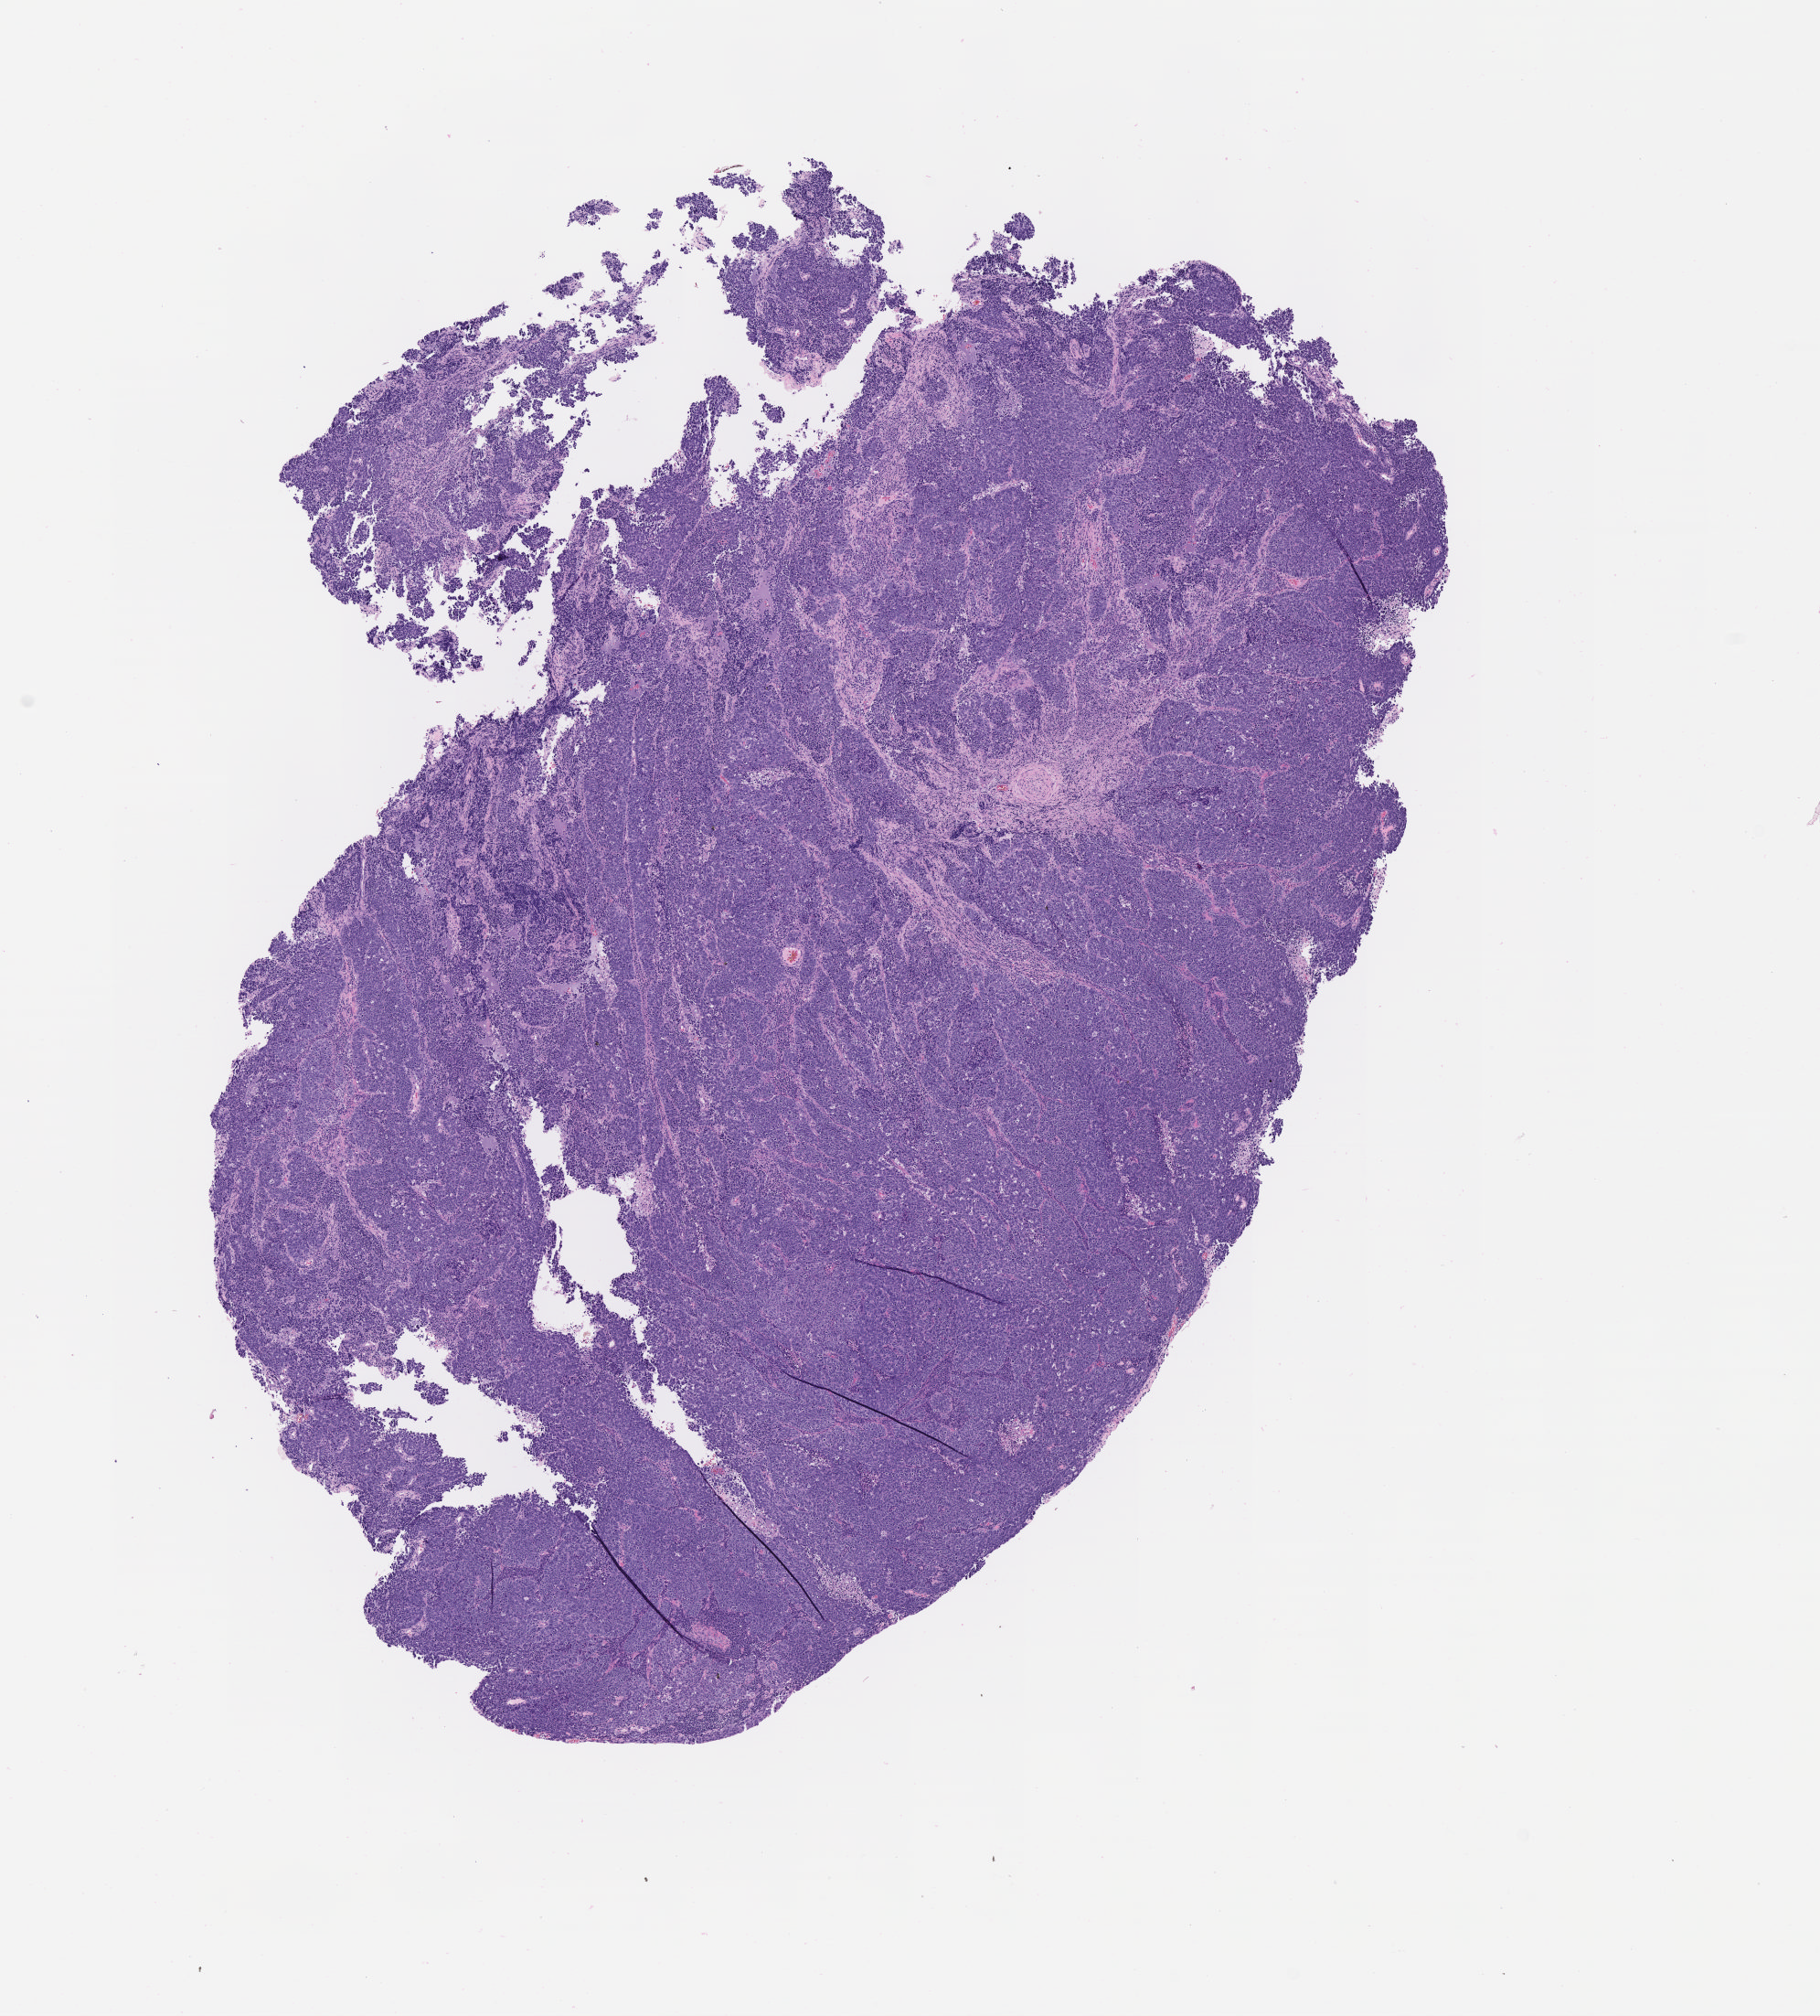
Whole-slide image, H&E stain, shown as a low-resolution overview of the whole scanned area (about 8.1 x 8.9 mm), tumor tissue, site: cervix. Female patient, age 40 years.
Histologic diagnosis: Small cell carcinoma, NOS.